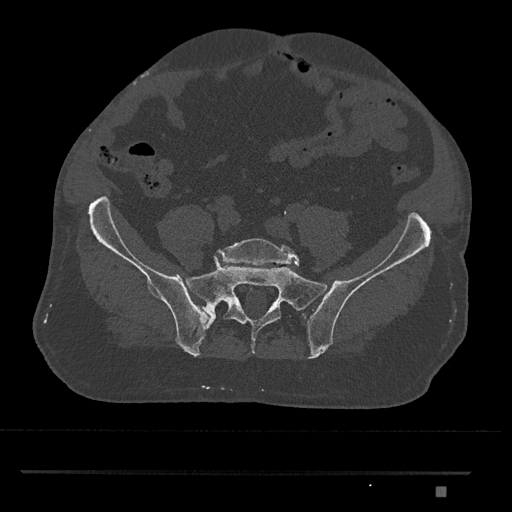
CT including the spine, one axial slice. Slice 513 of 1134 in the series (ordered by position). Reconstruction kernel Br40s/3. Bone window (W 1800 / L 400 HU). 512 × 512 image matrix, field of view 429 × 429 mm. Patient: male, 65 years. Case-level facts recorded for this patient, not image findings: primary cancer: prostate.
Structures marked on this image (semi-automatic segmentation, software-assisted and operator-edited):
- L5 vertebra: bounding box <216,238,300,266> (left, top, right, bottom; pixels)